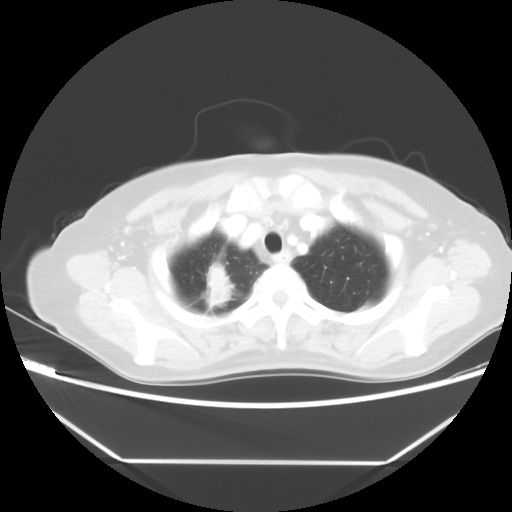
Chest CT, one axial slice. Slice 43 of 48 in the series (ordered by position). Lung window (W 1500 / L -600 HU). 512 × 512 image matrix, field of view 360 × 360 mm. Patient: female, 65 years. Case-level facts recorded for this patient, not image findings: clinical TNM (as recorded): T1c N1 M1.
Annotated regions visible in this slice (bounding box drawn by a radiologist):
- lung tumour (recorded histology: adenocarcinoma): bounding box (x1, y1, x2, y2) in pixels: (206, 259, 234, 308)